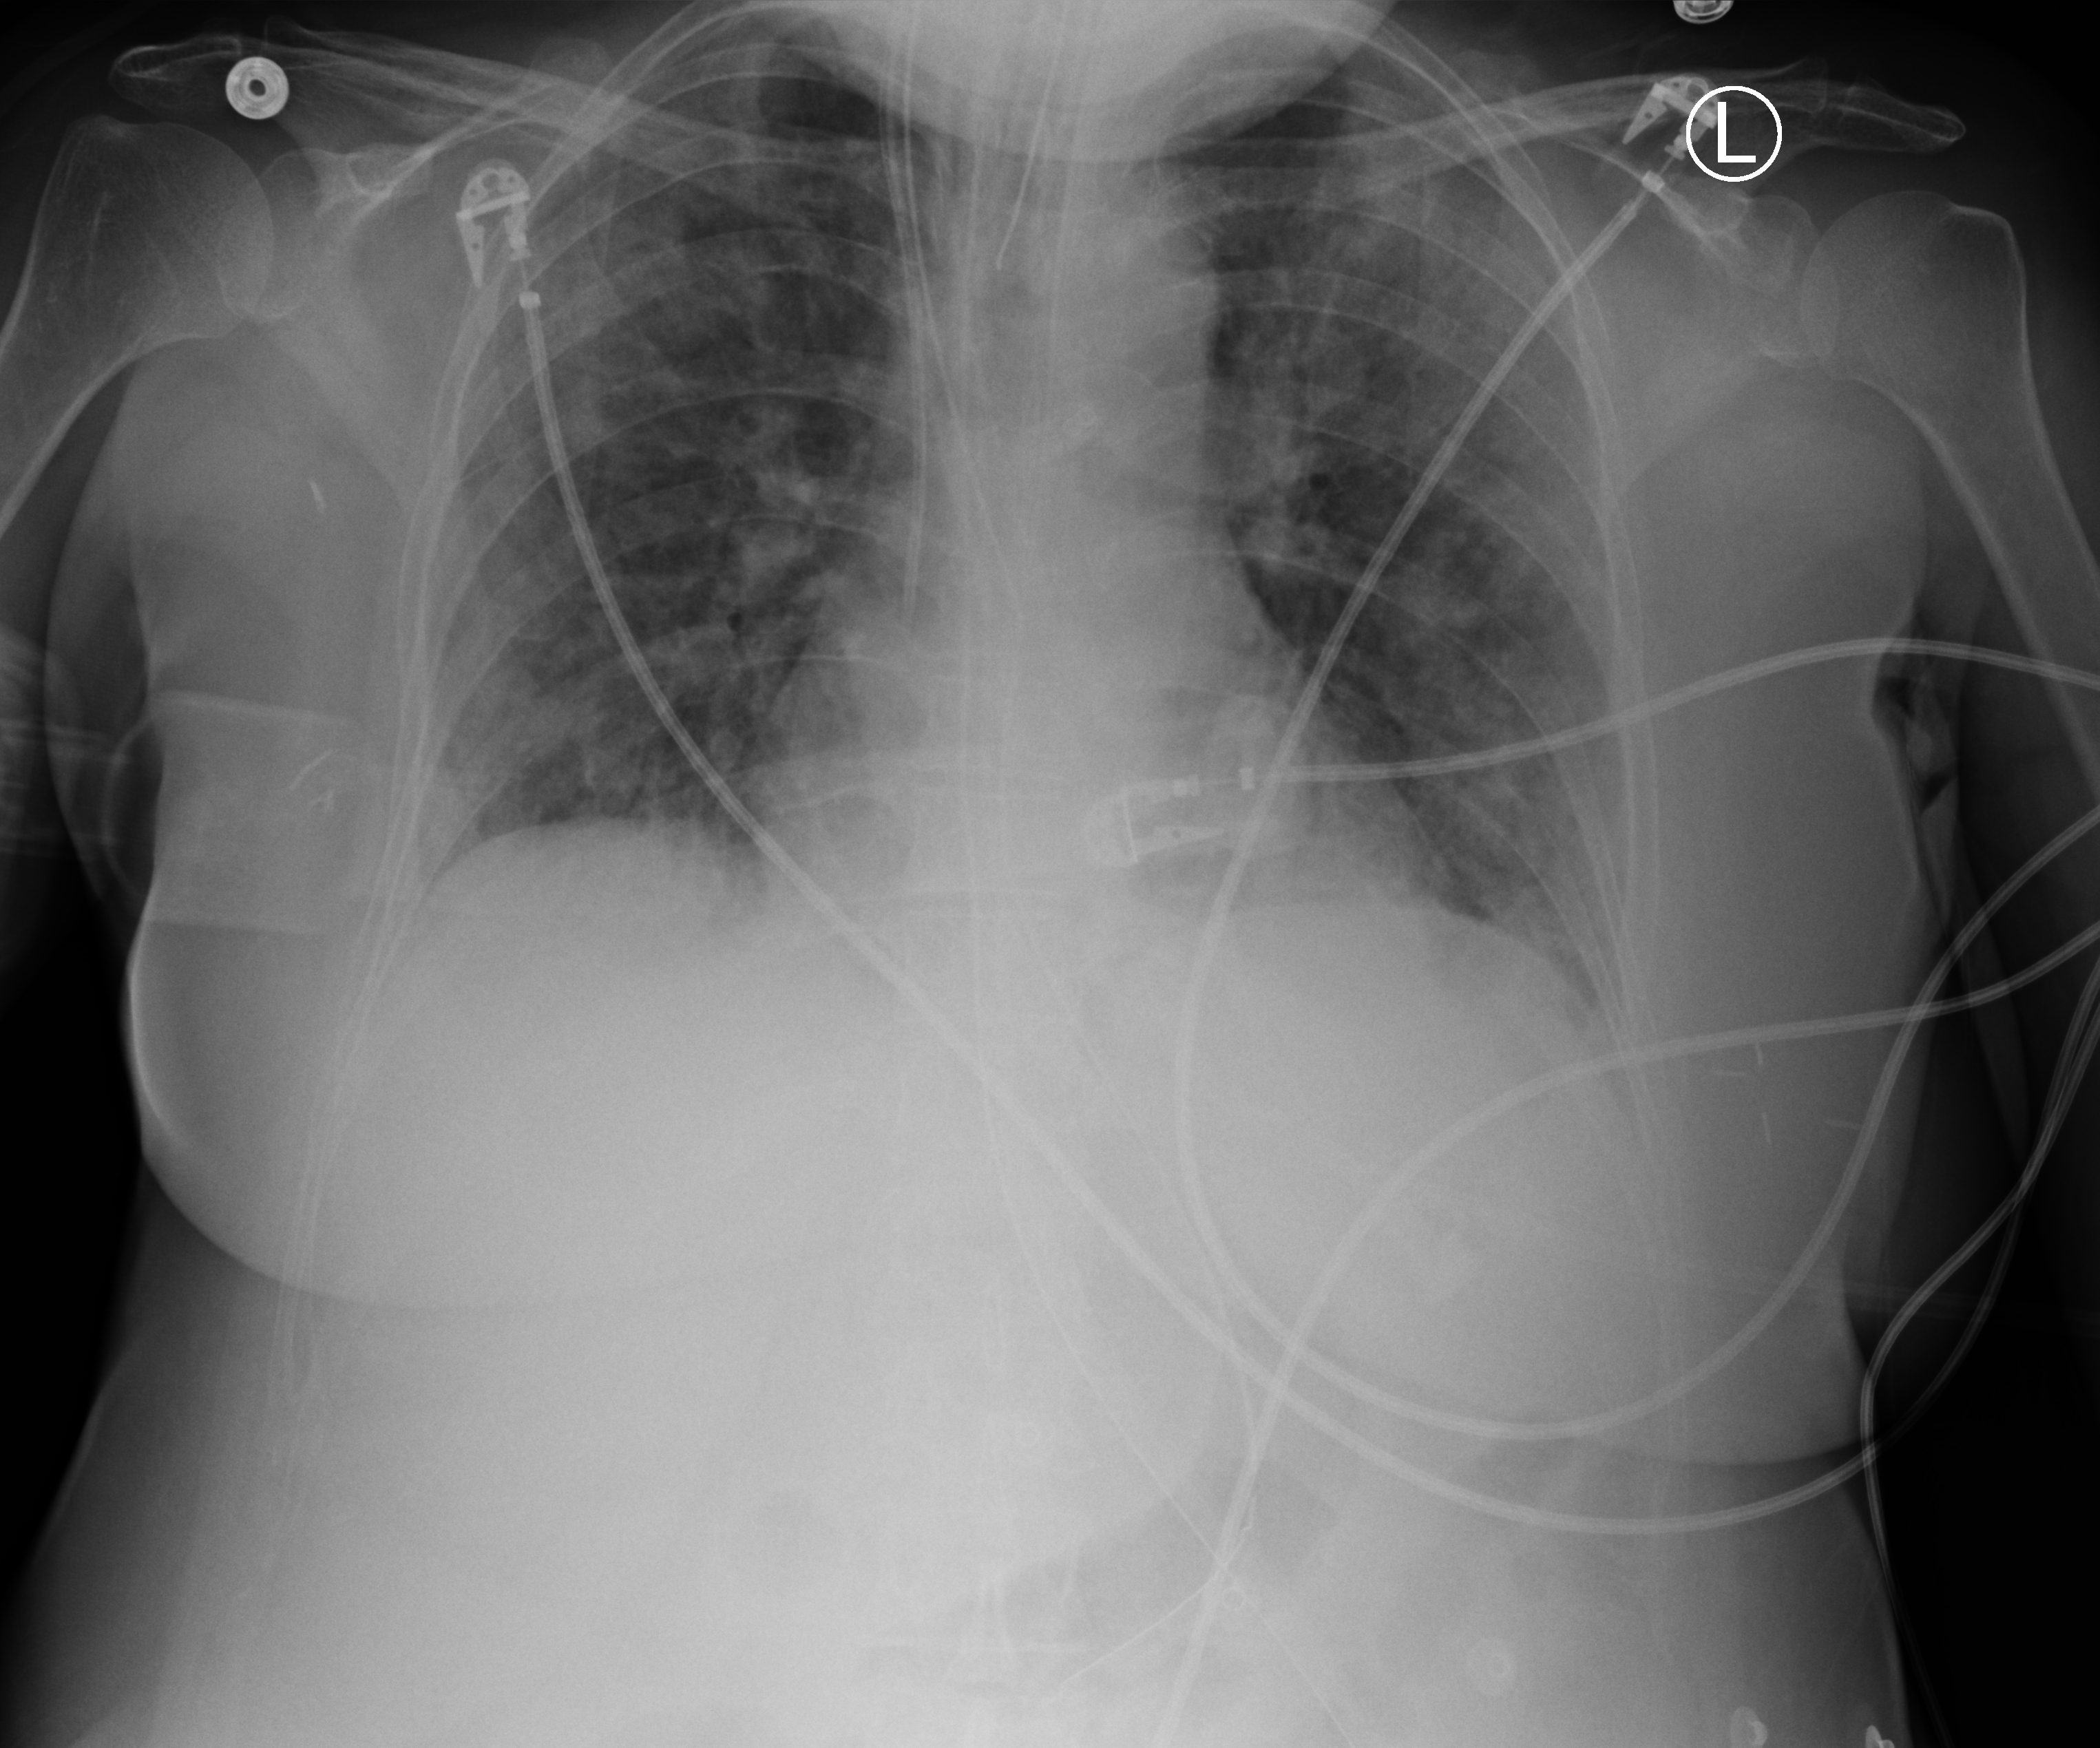
Bedside chest radiograph (computed radiography), anteroposterior (AP) projection. Female patient hospitalised with COVID-19, age 18–59 years.
Hospital-stay facts (about this admission, not read from this image; timing relative to this image not recorded):
- mechanically ventilated during this hospital stay: yes